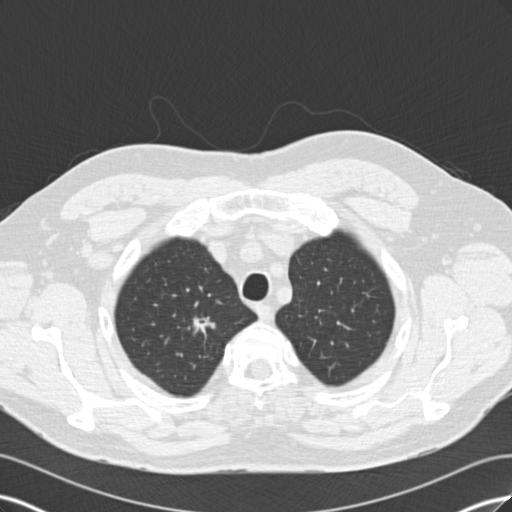
Low-dose screening chest CT, axial slice; baseline annual screen; lung window (W 1500 / L -600 HU); 2 mm slice thickness; standard (soft-tissue) reconstruction kernel (B30f). Male participant, aged 56 years at enrolment. Former smoker at enrolment.
Lesion marked by an expert reader, bounding box <173,306,226,350> (left, top, right, bottom; pixels). Reader record for this screening exam (exam-level; its link to the box is not recorded): non-calcified nodule or mass ≥4 mm, right upper lobe, 14 × 8 mm, spiculated (stellate) margins. Lung cancer was diagnosed 146 days after this screen: adenocarcinoma, NOS, right upper lobe, poorly differentiated (G3), stage IA (AJCC 6th edition), 12 mm at pathology.